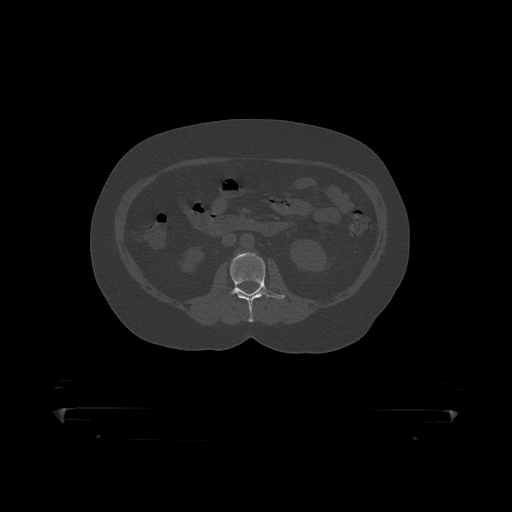
CT including the spine, one axial slice. Position 115 of 390 along the scan axis. 120 kVp. Bone window (W 1800 / L 400 HU). 512 × 512 image matrix, field of view 650 × 650 mm. Male patient, age 60 years. Case-level facts recorded for this patient, not image findings: primary cancer: prostate.
Outlined on this slice (semi-automatically segmented with operator editing):
- L2 vertebra: box from (x=221, y=253) to (x=285, y=319) px